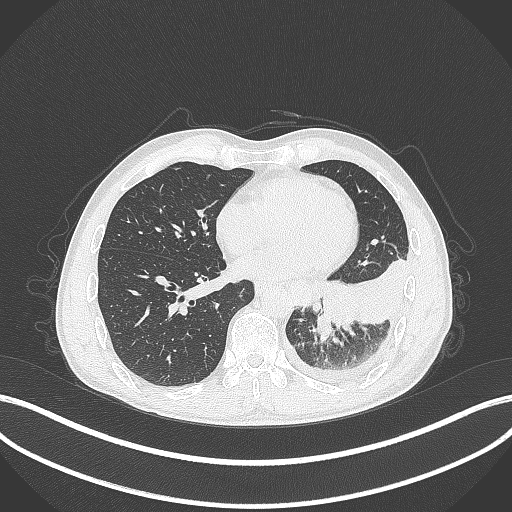
Chest CT, one axial slice. Position 110 of 295 along the scan axis. Reconstruction kernel B70f. 120 kVp. Lung window (W 1500 / L -600 HU). 1 mm slice thickness. 512 × 512 image matrix. Patient: male, 47 years. Case-level facts recorded for this patient, not image findings: clinical TNM (as recorded): T3 N1 M1c; histopathological grade: G3.
Annotated regions visible in this slice (rectangle marked by the reading radiologist):
- lung tumour (recorded histology: small cell carcinoma): box from (x=310, y=311) to (x=333, y=342) px